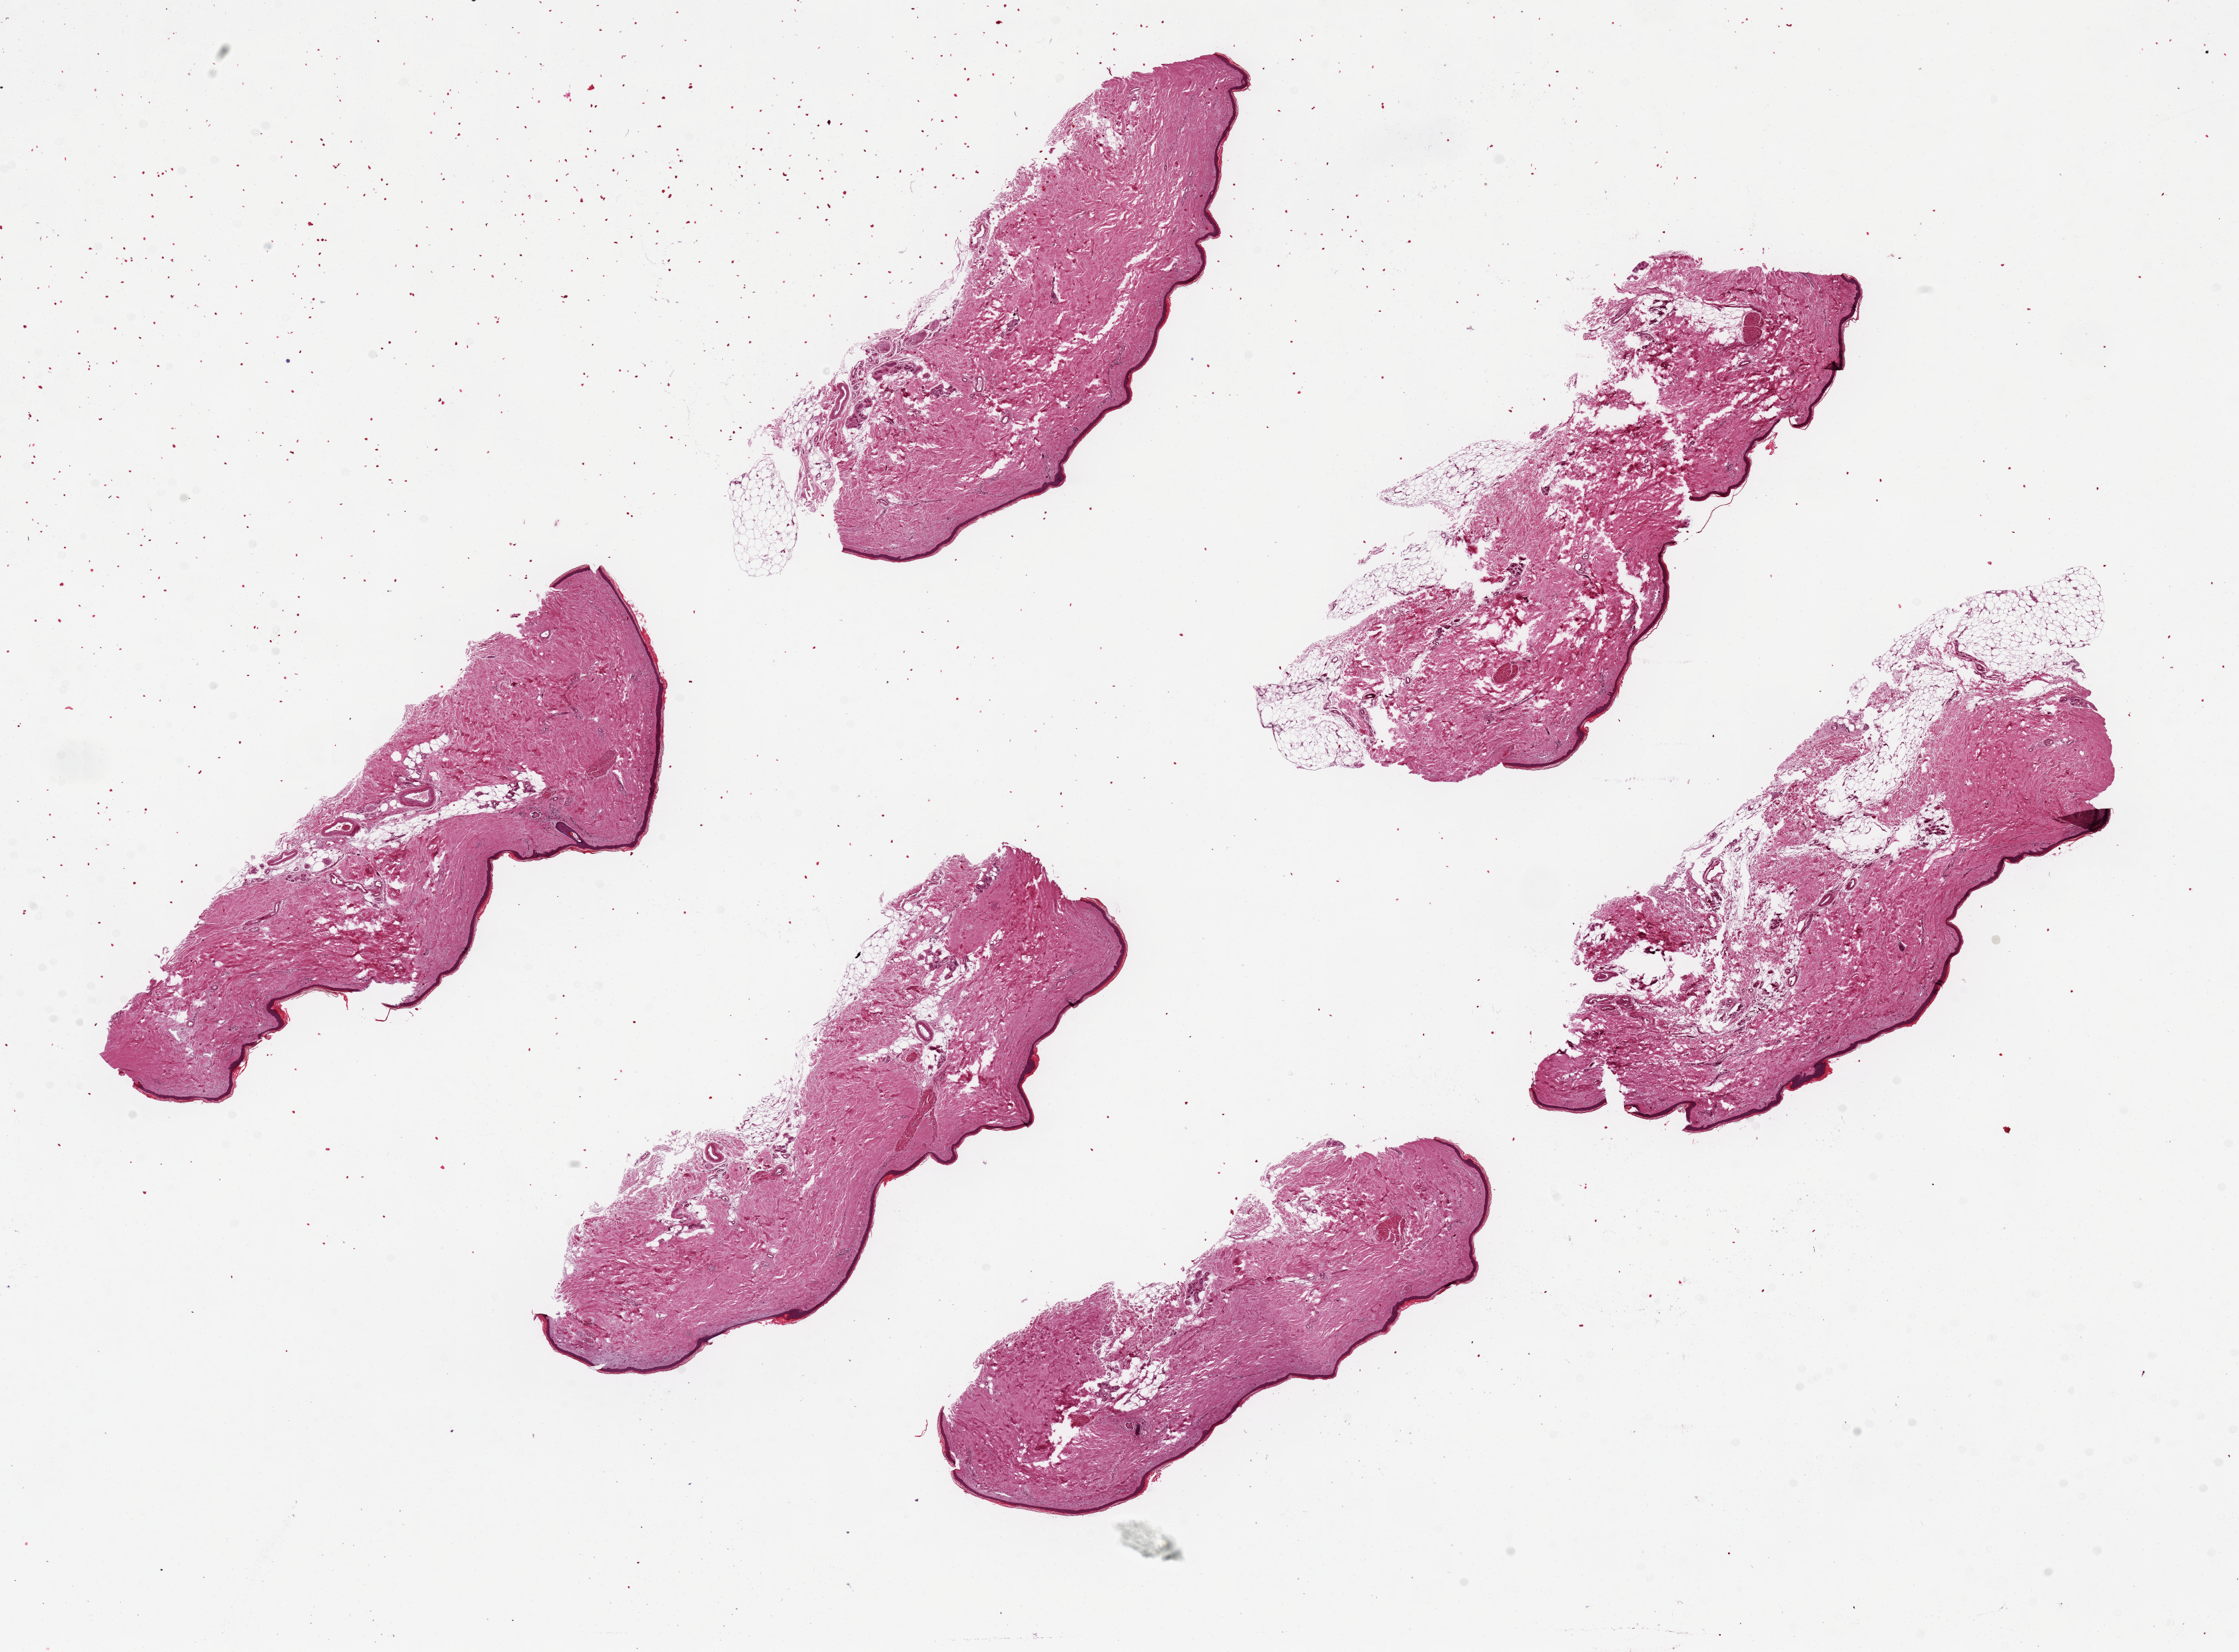
Whole-slide image, H&E stain — low-resolution overview of the scanned area, about 26.6 x 19.6 mm, PAXgene-fixed paraffin-embedded (PFPE) section, section of skin of lower leg (target tissue), tissue donor sample.
Reviewer comment on this tissue sample: 6 pieces up to 9X3 mm.